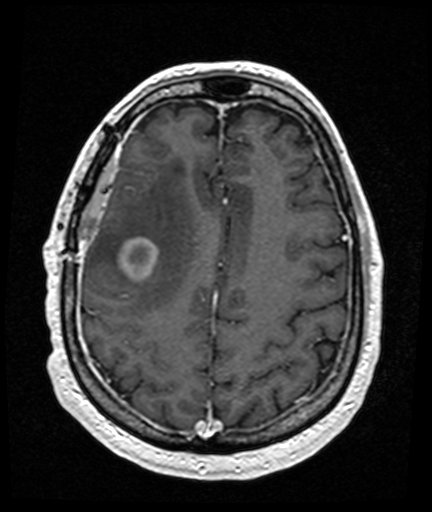
Brain MRI from a brain-tumour surgery series, one axial slice; slice 50 of 176 in the series (ordered by position); T1-weighted post-contrast; 1 mm slice thickness; 432 × 512 image matrix. From the clinical record (not read from this slice): histopathology: Glioblastoma; WHO grade: 4; IDH mutation: no; tumour location: Right Frontal Temporal, Posterior Sylvian Fissure.
Structures marked on this image (expert manual segmentation):
- tumour: box from (x=121, y=238) to (x=157, y=280) px